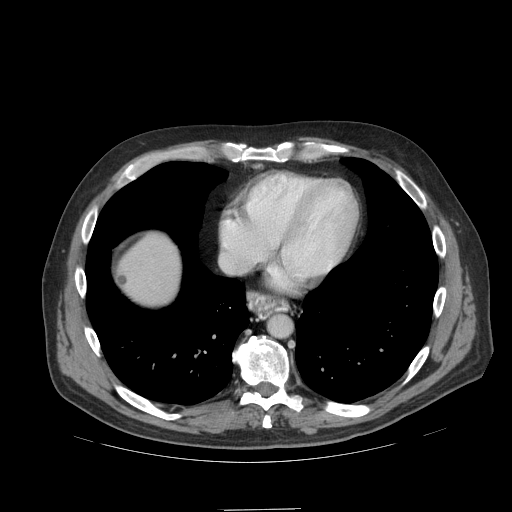
Contrast-enhanced abdominal CT (liver protocol), one axial slice. Slice 95 of 99 in the series (ordered by position). Reconstruction kernel STANDARD. 140 kVp. Soft-tissue window (W 400 / L 40 HU). 2.5 mm slice thickness. 512 × 512 image matrix, field of view 440 × 440 mm. From the clinical record (not read from this slice): diagnosis: hepatocellular carcinoma (patient treated with transarterial chemoembolisation; whether this scan precedes or follows treatment is not stated here); TNM stage (as recorded): Stage-I; Child-Pugh class: A.
Annotated regions visible in this slice (semi-automatically segmented with operator editing):
- abdominal aorta: bounding box <269,315,291,337> (left, top, right, bottom; pixels)
- liver parenchyma outside the tumour (the mass and vessels are separate outlines, so this box may not span the whole liver): <120,234,180,304>